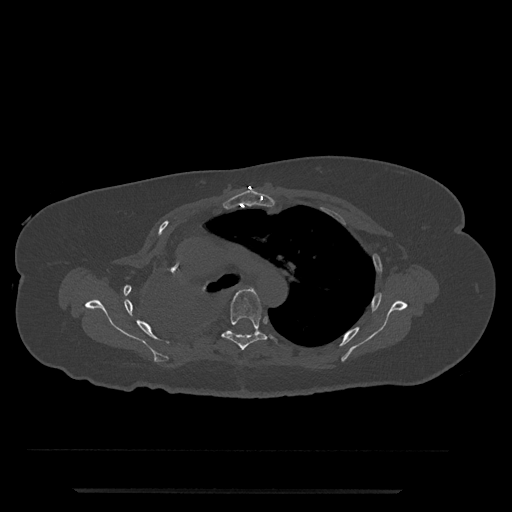
CT including the spine, one axial slice; slice 545 of 797 in the series (ordered by position); reconstruction kernel Br40s/3; 120 kVp; bone window (W 1800 / L 400 HU); 0.5 mm slice thickness; 512 × 512 image matrix, field of view 440 × 440 mm. Patient: female, 51 years. From the clinical record (not read from this slice): primary cancer: neuro.
Annotated regions visible in this slice (semi-automatically segmented with operator editing):
- T5 vertebra: bounding box <222,289,274,350> (left, top, right, bottom; pixels)